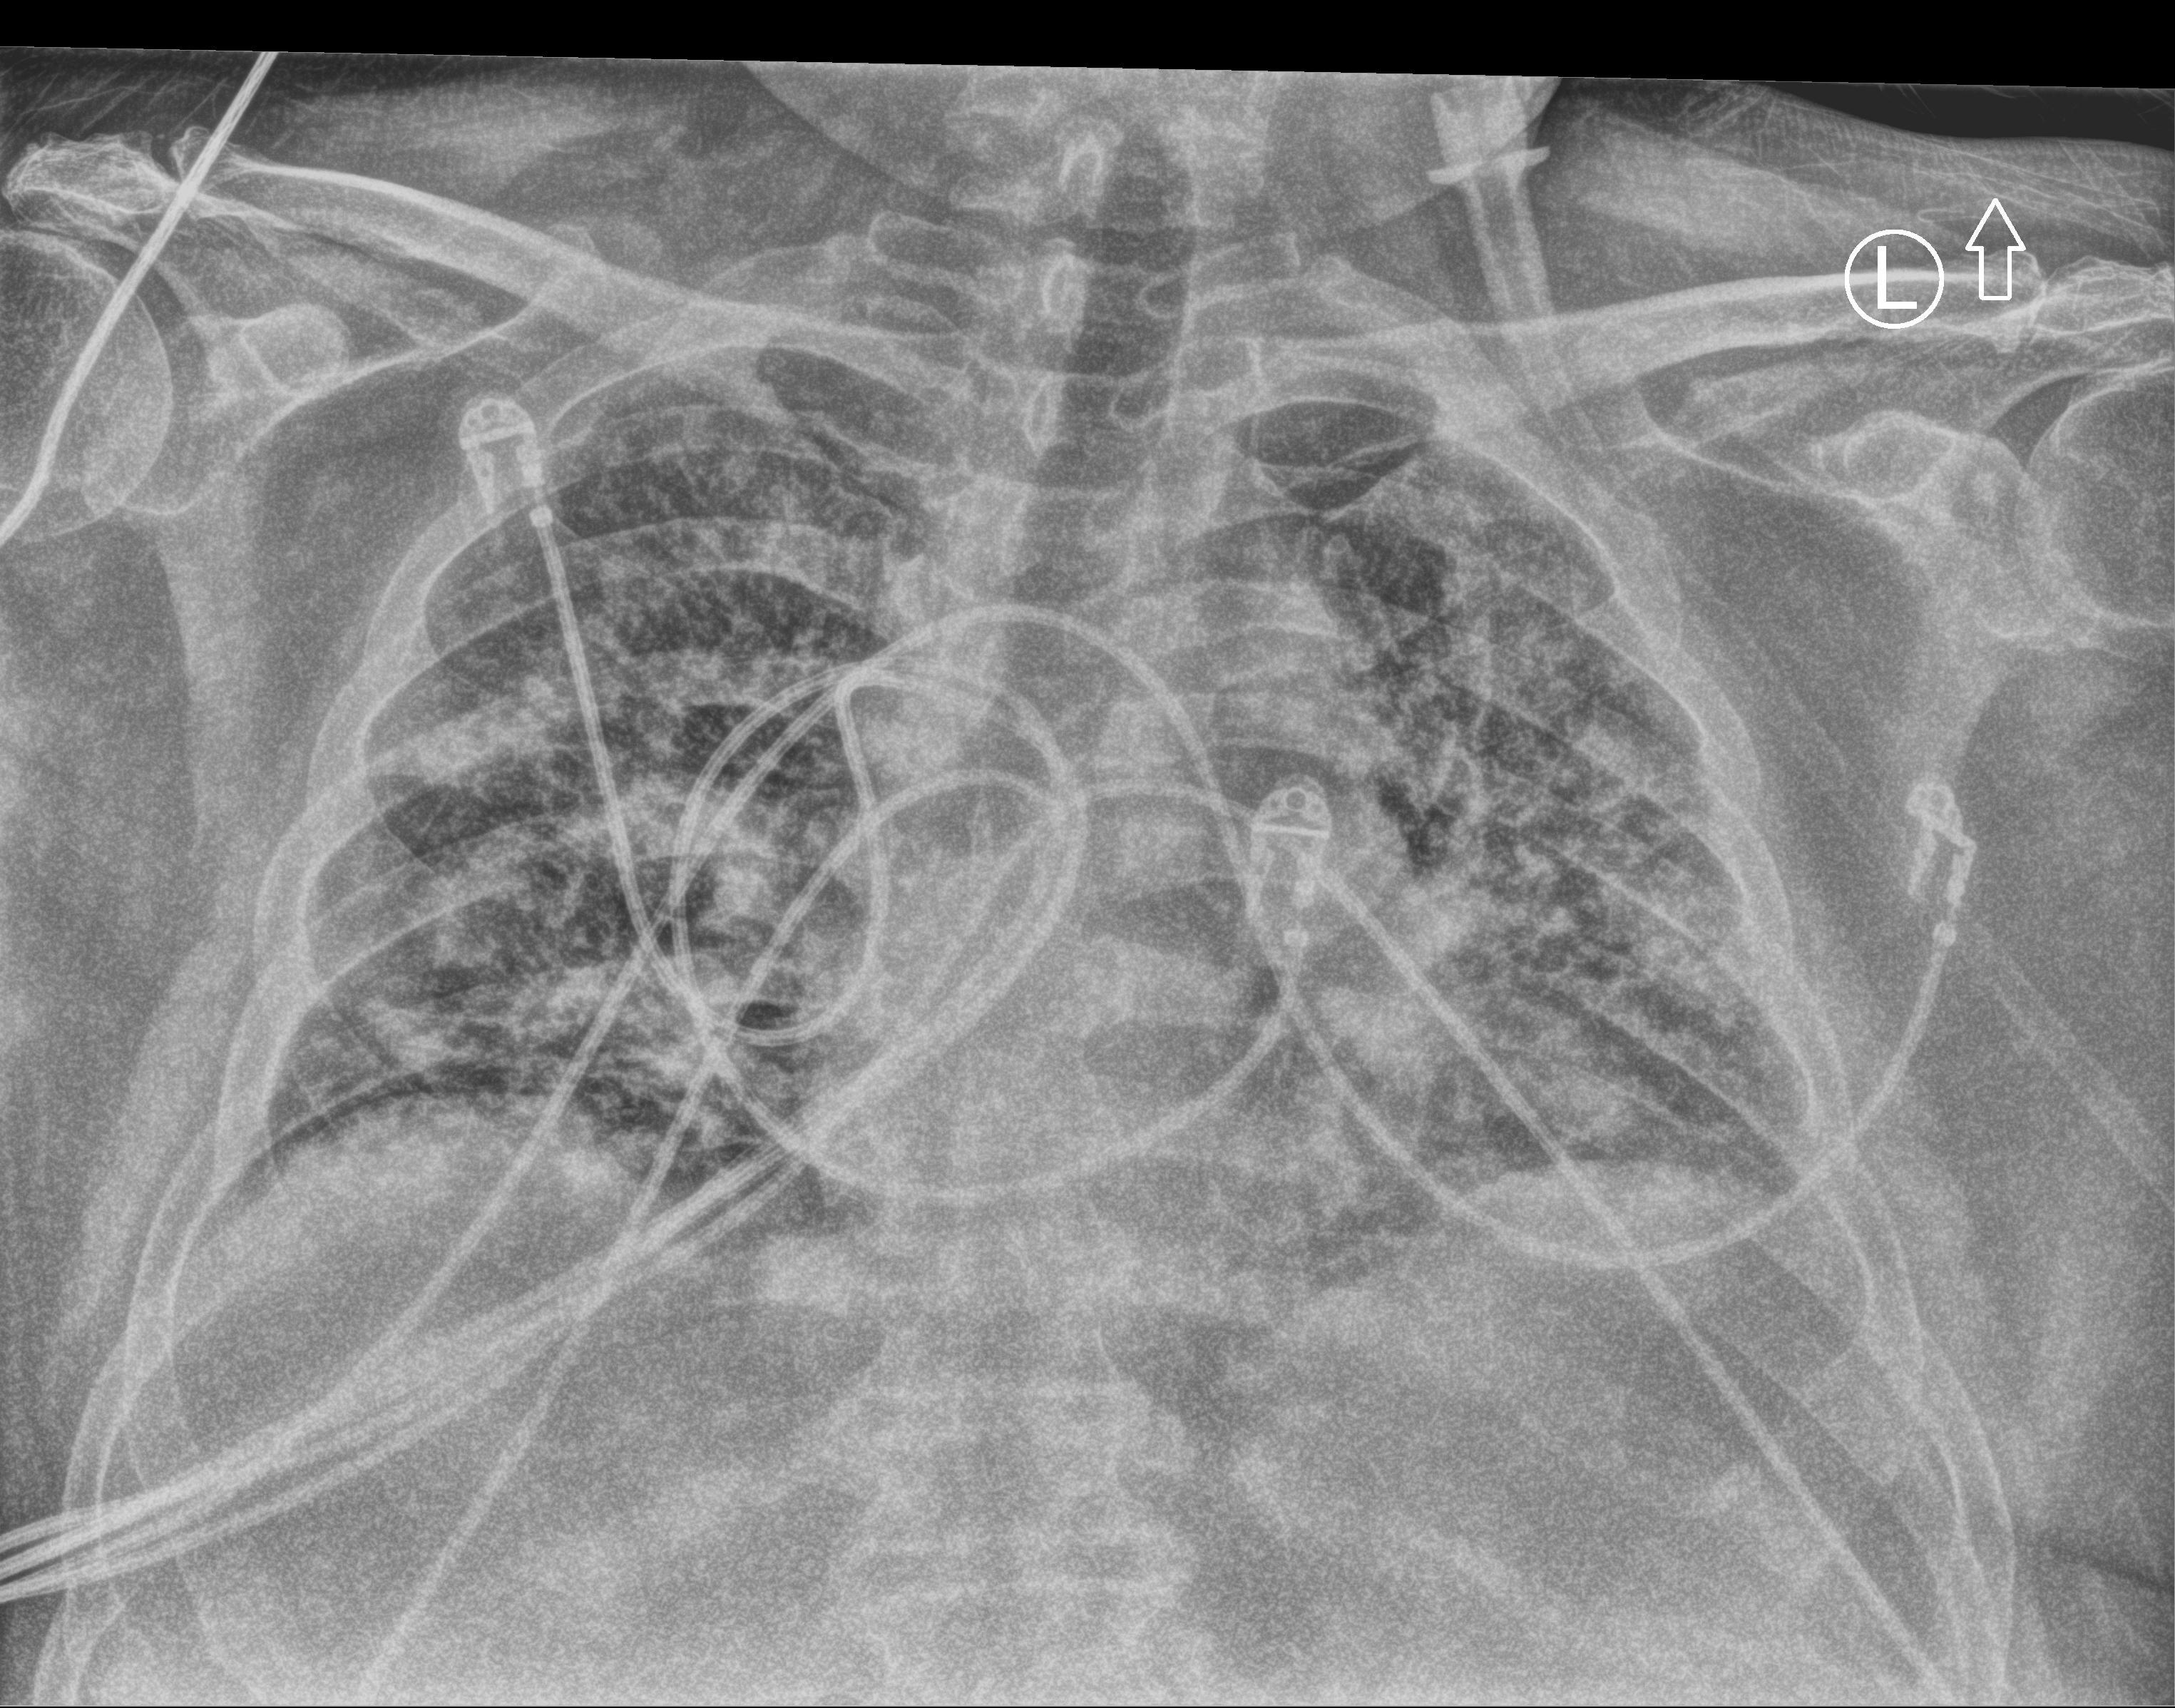
Bedside chest radiograph (computed radiography); anteroposterior (AP) projection. Patient hospitalised with COVID-19; male, aged 18–59 years.
Hospital-stay facts (about this admission, not read from this image; timing relative to this image not recorded): length of hospital stay: 25 days; mechanically ventilated during this hospital stay: no; COPD (admission record): no.